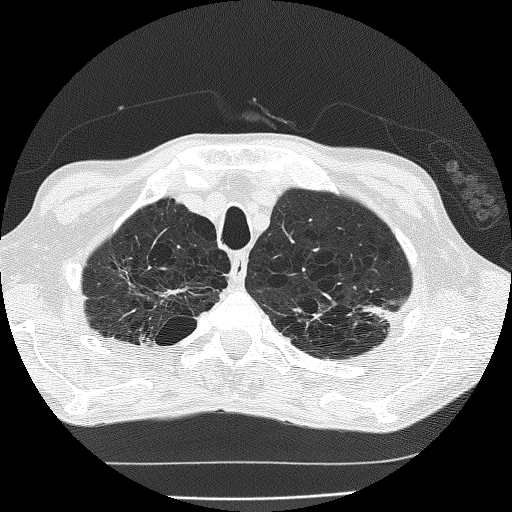
Chest CT (low-dose screening protocol), one axial image. Second annual screen. Lung window (W 1500 / L -600 HU). Lung (sharp) reconstruction kernel (FC51). 120 kVp. Male, age 60 years at enrolment. Current smoker at enrolment.
Expert reader's lesion annotation, bounding box <346,282,413,344> (left, top, right, bottom; pixels). The screening reader recorded 2 non-calcified nodules or masses ≥4 mm on this exam (left upper lobe, left upper lobe); which of them this box marks is not recorded. Official screen result: positive, other.